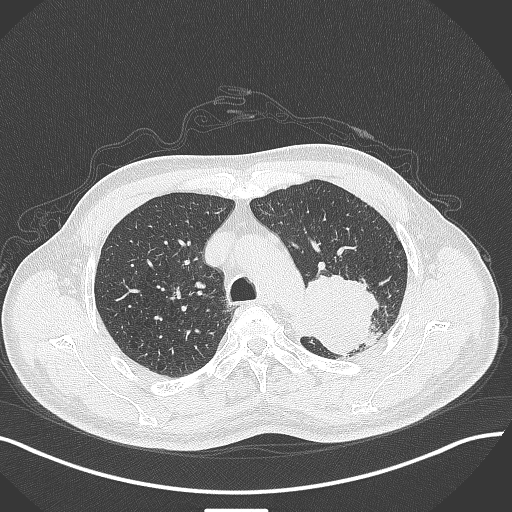
Chest CT, one axial slice. Slice 318 of 429 in the series (ordered by position). 120 kVp. Lung window (W 1500 / L -600 HU). 1 mm slice thickness. 512 × 512 image matrix, field of view 400 × 400 mm. Male patient, age 55 years. Case-level facts recorded for this patient, not image findings: clinical TNM (as recorded): T3 N0 M1c; histopathological grade: G3.
Structures marked on this image (bounding box drawn by a radiologist):
- lung tumour (recorded histology: adenocarcinoma): bounding box (x1, y1, x2, y2) in pixels: (294, 271, 383, 360)